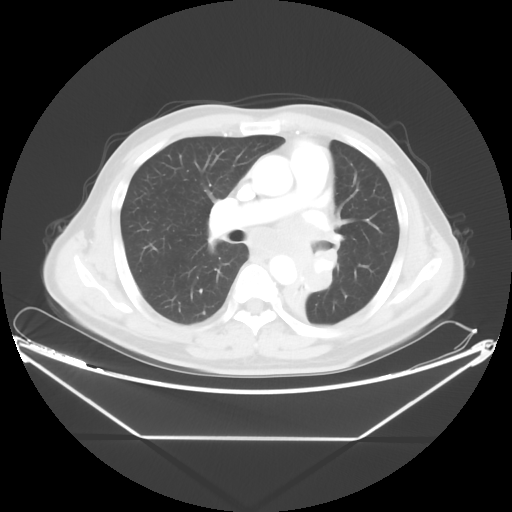
Chest CT, one axial slice; slice 26 of 48 in the series (ordered by position); reconstruction kernel STANDARD; lung window (W 1500 / L -600 HU); 5 mm slice thickness; 512 × 512 image matrix, field of view 438 × 438 mm. Male patient, age 58 years. From the clinical record (not read from this slice): clinical TNM (as recorded): T3 N3 M0.
Annotated regions visible in this slice (bounding box drawn by a radiologist):
- lung tumour (recorded histology: squamous cell carcinoma): bounding box [x1, y1, x2, y2] px = [284, 248, 342, 316]